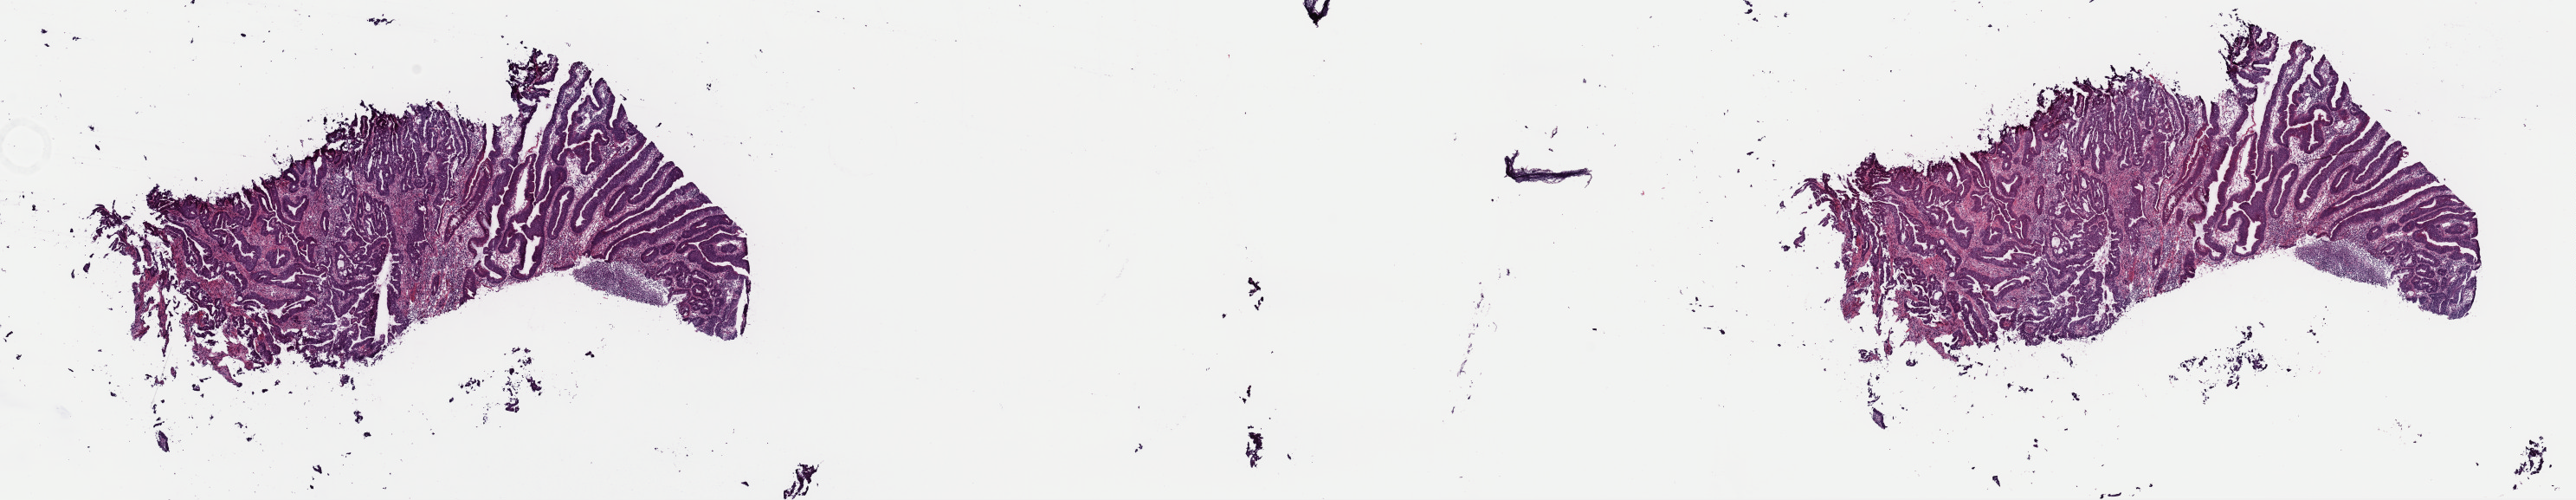
H&E whole-slide image — shown as a low-resolution overview of the whole scanned area (about 23.5 x 4.6 mm, acquisition: 40x scan), frozen section from the top of the tissue portion, colon, primary tumour sample. Male patient; age at initial diagnosis 61 years. Pathologist review of this section (percent, as recorded): tumour cells 100%, tumour nuclei 65%, normal cells 0%, stromal cells 0%, necrosis 0%. Infiltration values recorded for this section: lymphocyte infiltration 15%, monocyte infiltration 1%, neutrophil infiltration 1%.
* lymph nodes positive (case pathology): 0 of 23 examined
* diagnosis: Adenocarcinoma, NOS (cecum)
* AJCC pathologic stage: I (7th edition)